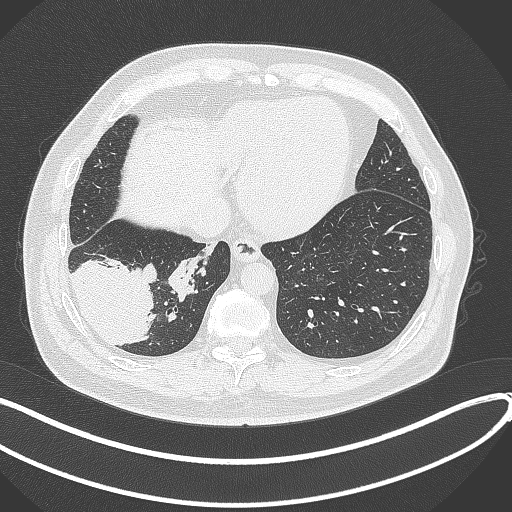
Chest CT, one axial slice. Slice 89 of 360 in the series (ordered by position). Reconstruction kernel B70f. 120 kVp. Lung window (W 1500 / L -600 HU). 1 mm slice thickness. 512 × 512 image matrix. Male patient, age 59 years.
Outlined on this slice (rectangle marked by the reading radiologist):
- lung tumour (recorded histology: adenocarcinoma): bounding box <68,249,157,351> (left, top, right, bottom; pixels)